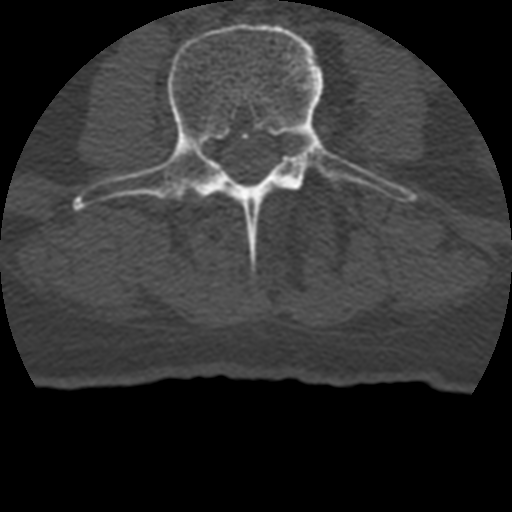
CT including the spine, one axial slice; position 91 of 399 along the scan axis; reconstruction kernel STANDARD; 120 kVp; bone window (W 1800 / L 400 HU); 1.25 mm slice thickness; 512 × 512 image matrix, field of view 160 × 160 mm. Patient age 69 years. Case-level facts recorded for this patient, not image findings: primary cancer: prostate.
Outlined on this slice (semi-automatic segmentation, software-assisted and operator-edited):
- L3 vertebra: bounding box (x1, y1, x2, y2) in pixels: (77, 23, 413, 224)